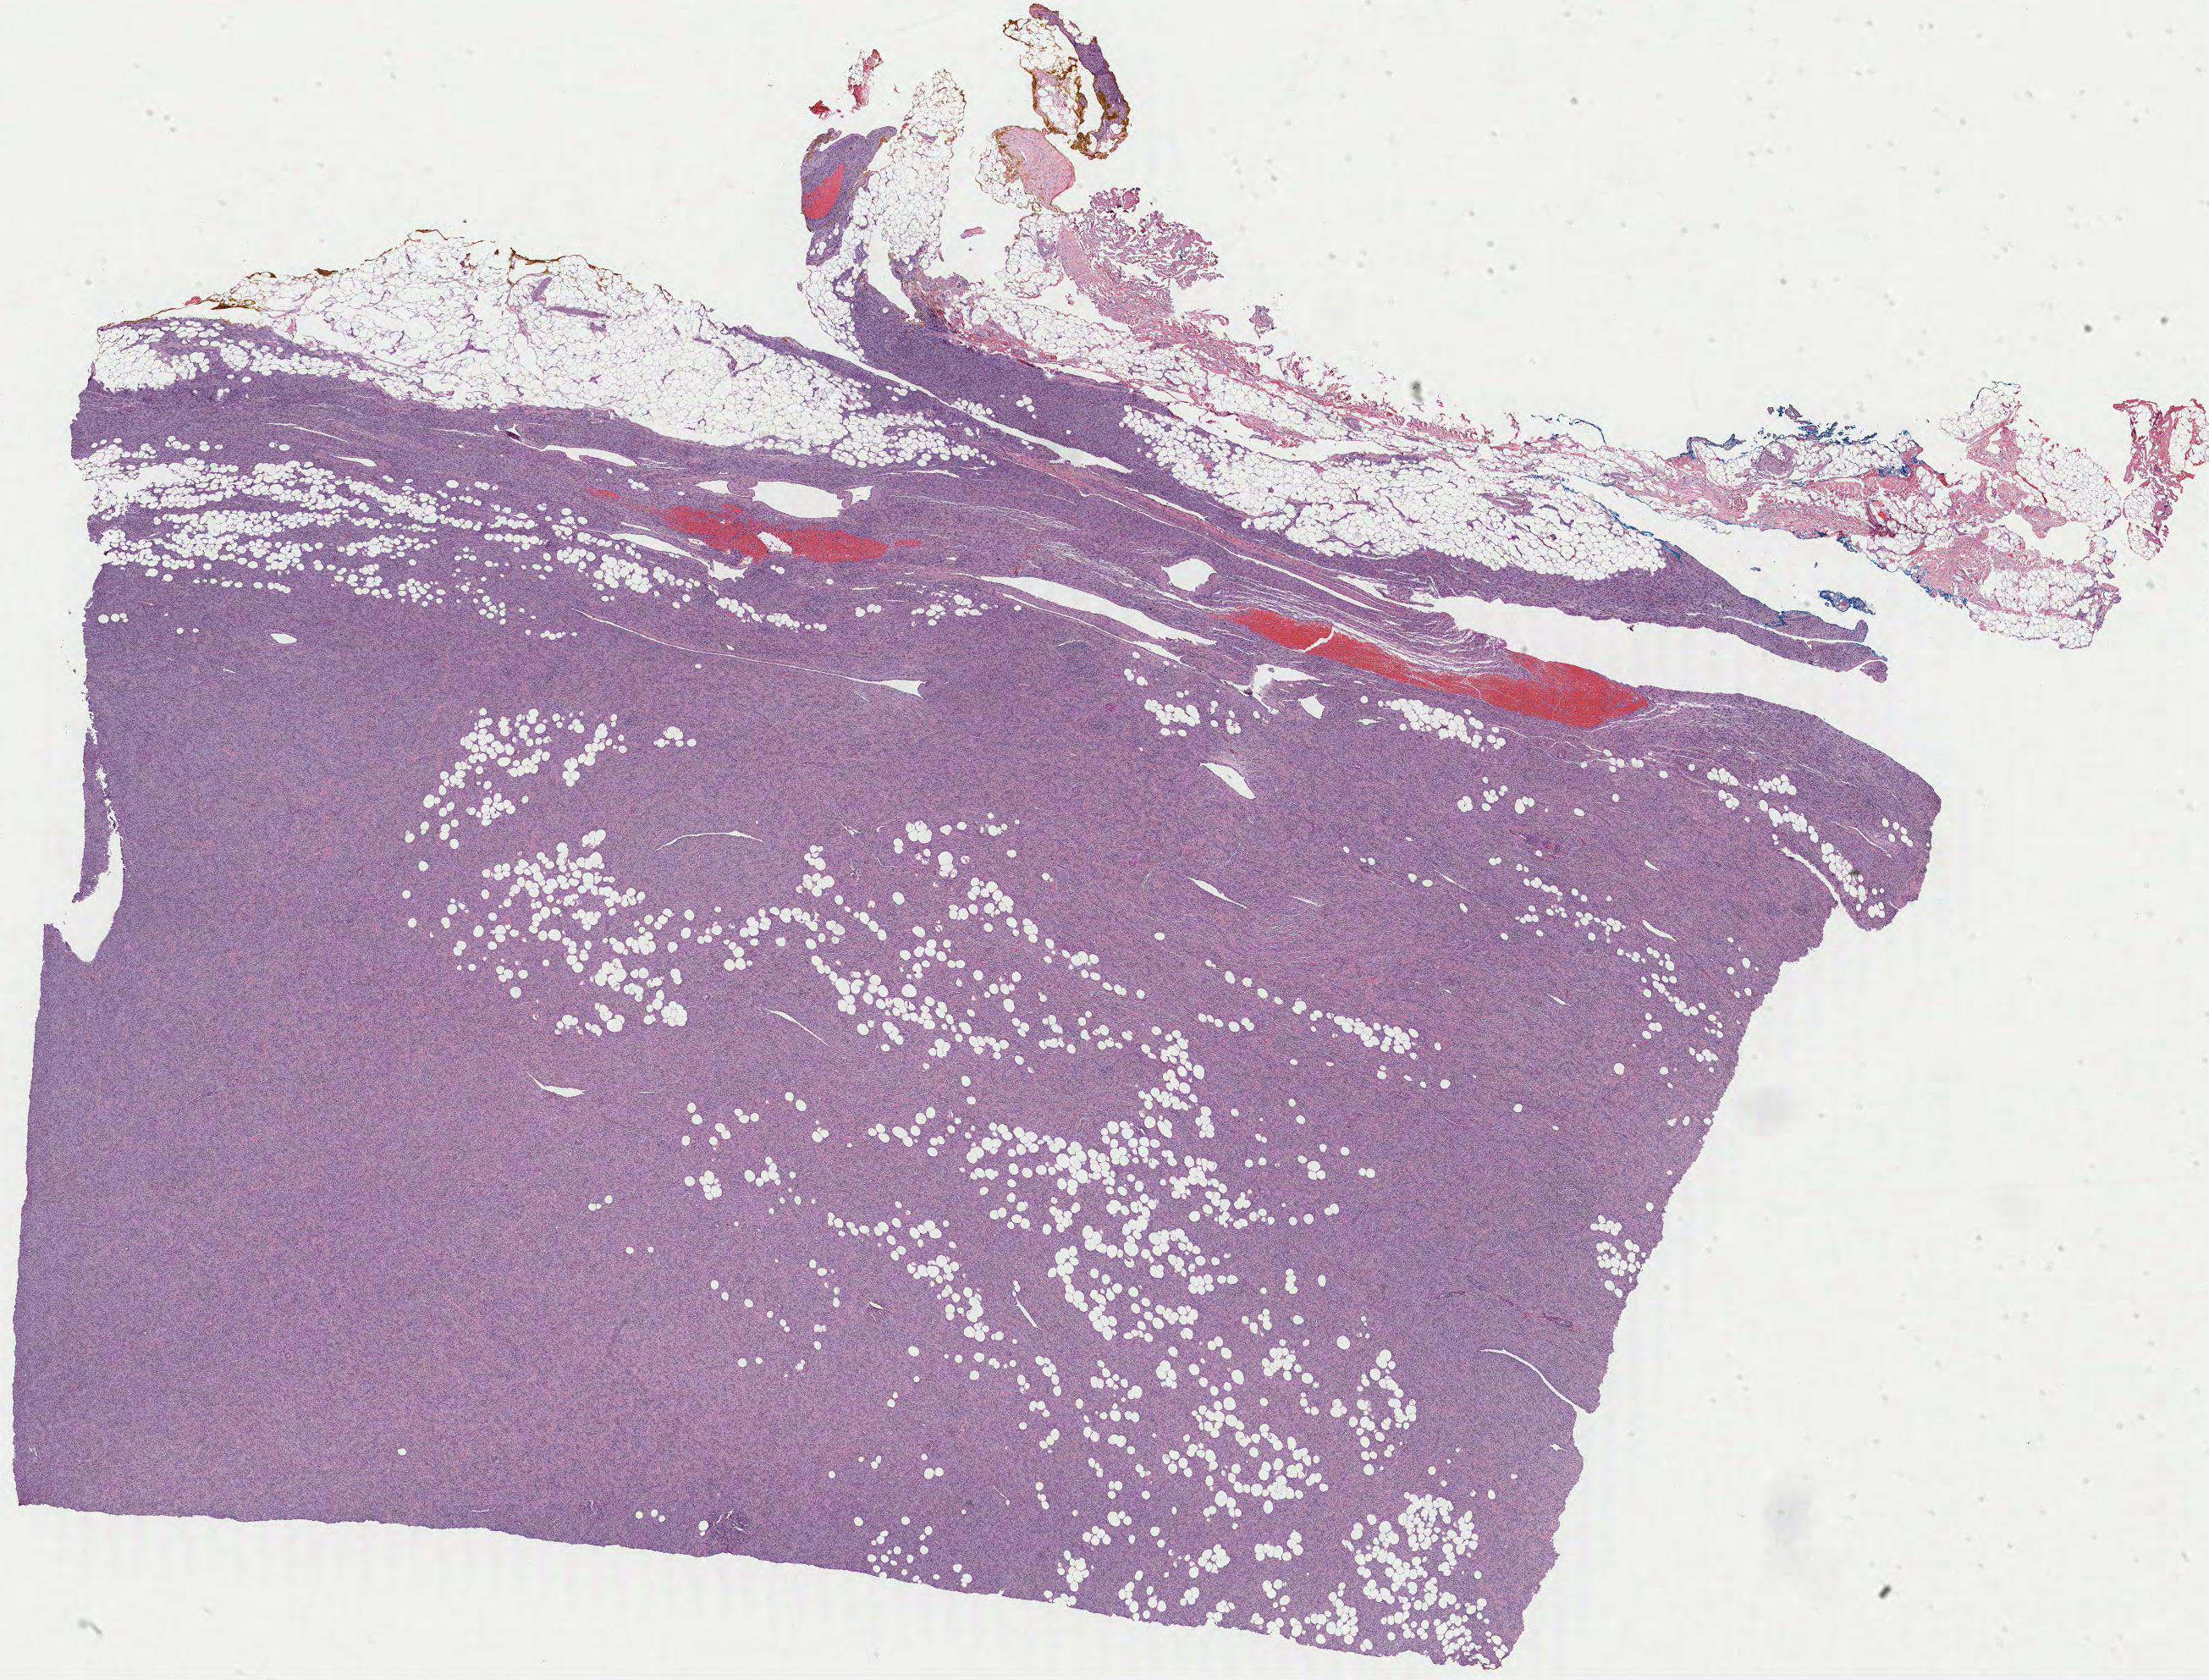
Digitized H&E tissue section (whole slide) — shown as a low-resolution overview of the whole scanned area (about 20.9 x 15.9 mm), formalin-fixed paraffin-embedded (FFPE) diagnostic section, metastatic tumour sample, sampled site not recorded. Patient: male, age at initial diagnosis 26 years.
This section: metastatic tumour tissue. Patient diagnosis: Spindle cell melanoma, NOS.